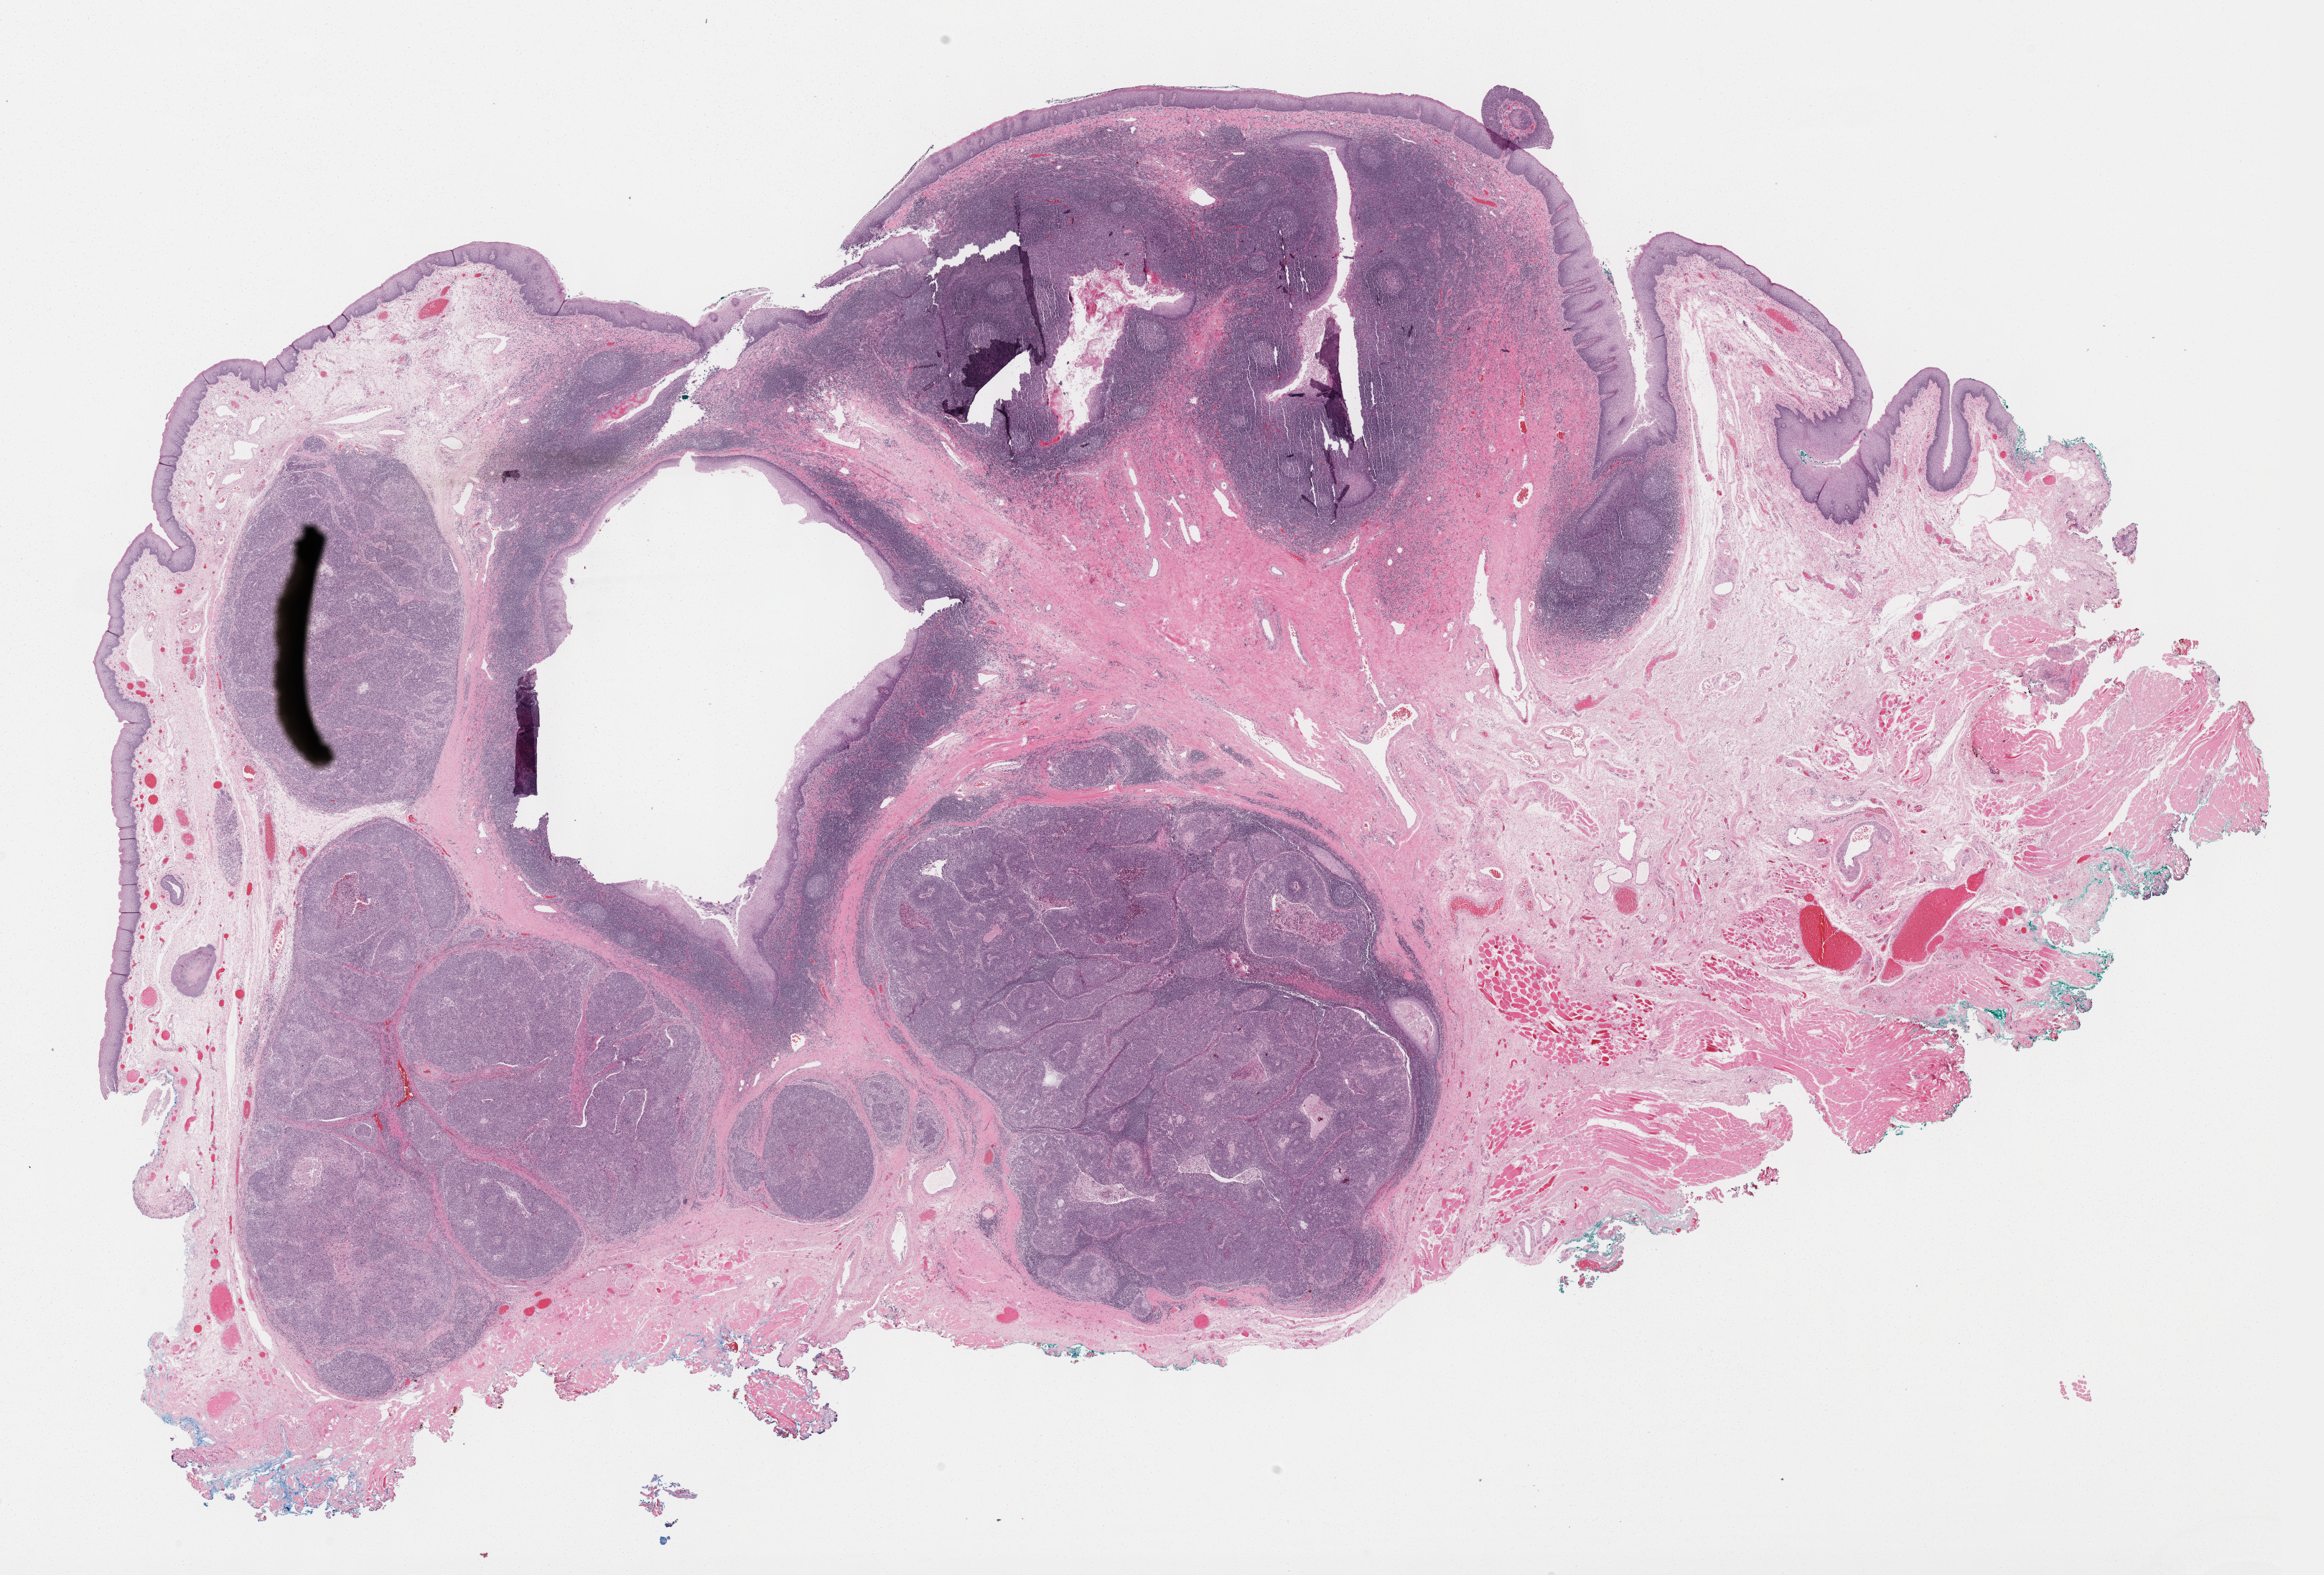
Whole-slide histology image, H&E-stained, shown as a low-resolution overview of the whole scanned area (about 26.2 x 17.7 mm); formalin-fixed paraffin-embedded (FFPE) diagnostic section; head and neck, primary tumour sample. Male, age 58 years at initial diagnosis. Histologic grade: G3 (poorly differentiated).
Laterality: left. Pathologic diagnosis: Squamous cell carcinoma, large cell, nonkeratinizing, NOS (tonsil, NOS). AJCC pathologic stage: II.